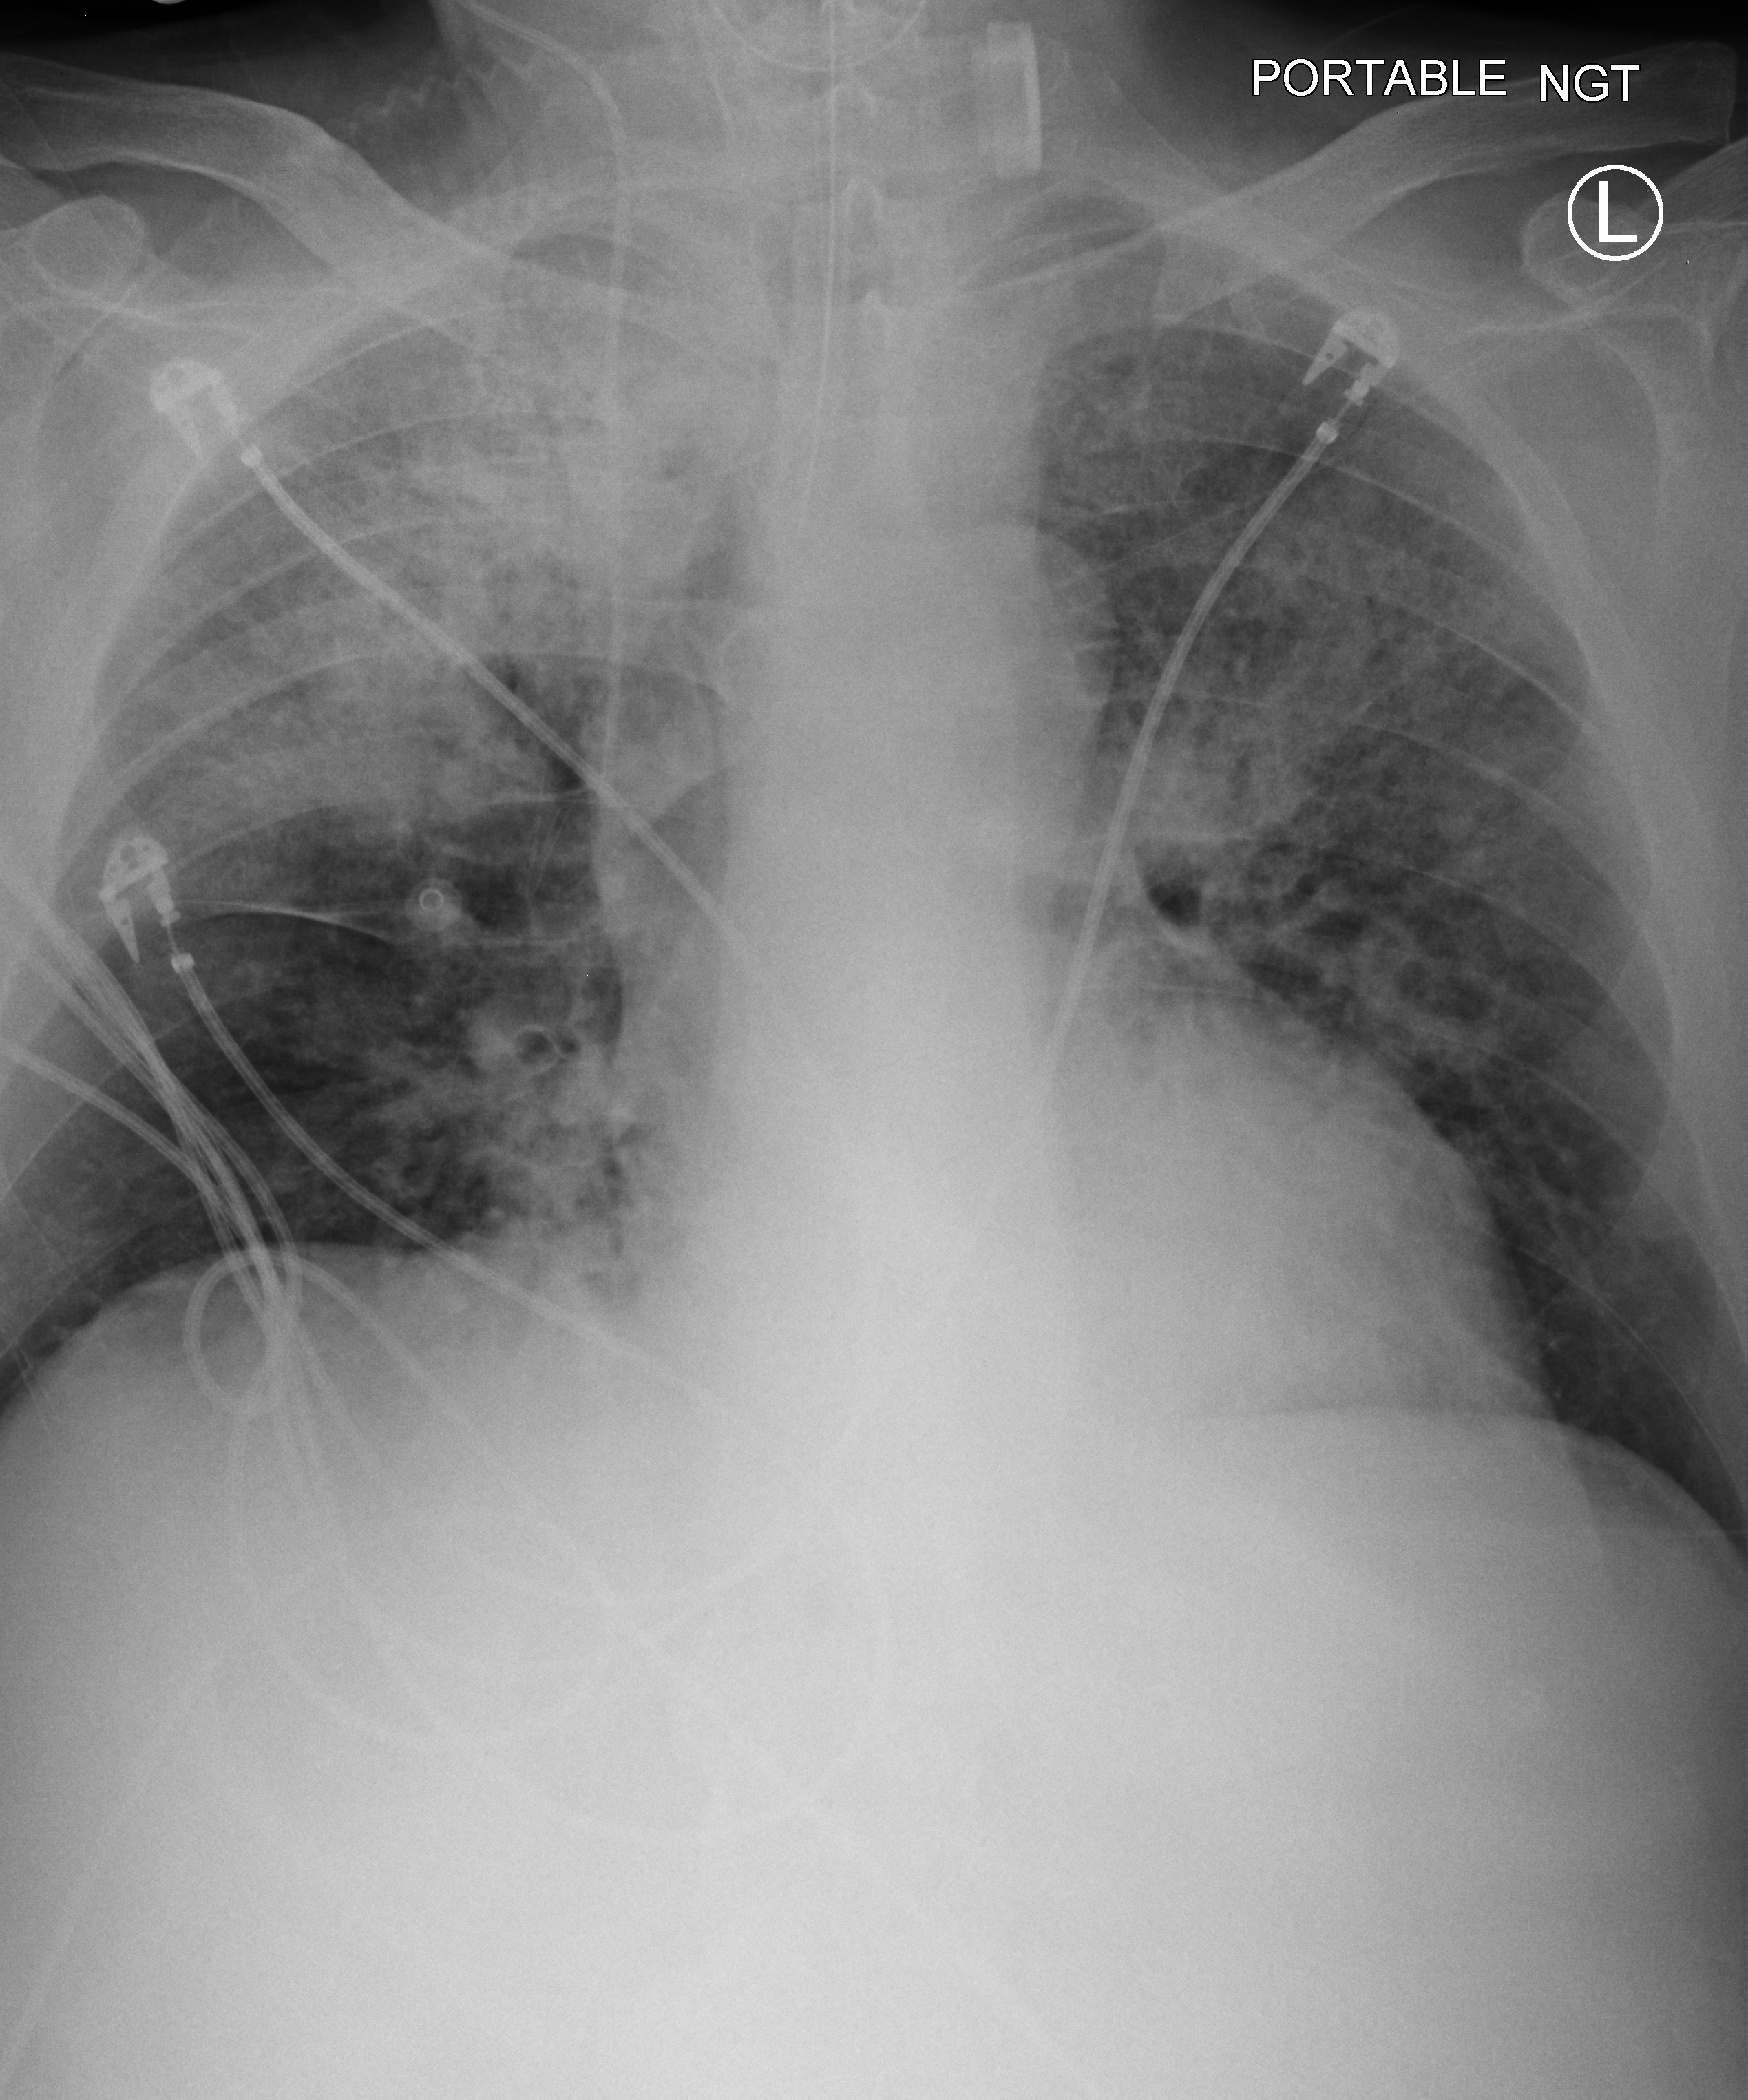
Portable chest radiograph, anteroposterior (AP) projection. Male patient hospitalised with COVID-19, age 75–90 years.
Hospital-stay facts (about this admission, not read from this image; timing relative to this image not recorded): length of hospital stay: 2 days; hypertension (admission record): no; mechanically ventilated during this hospital stay: yes.